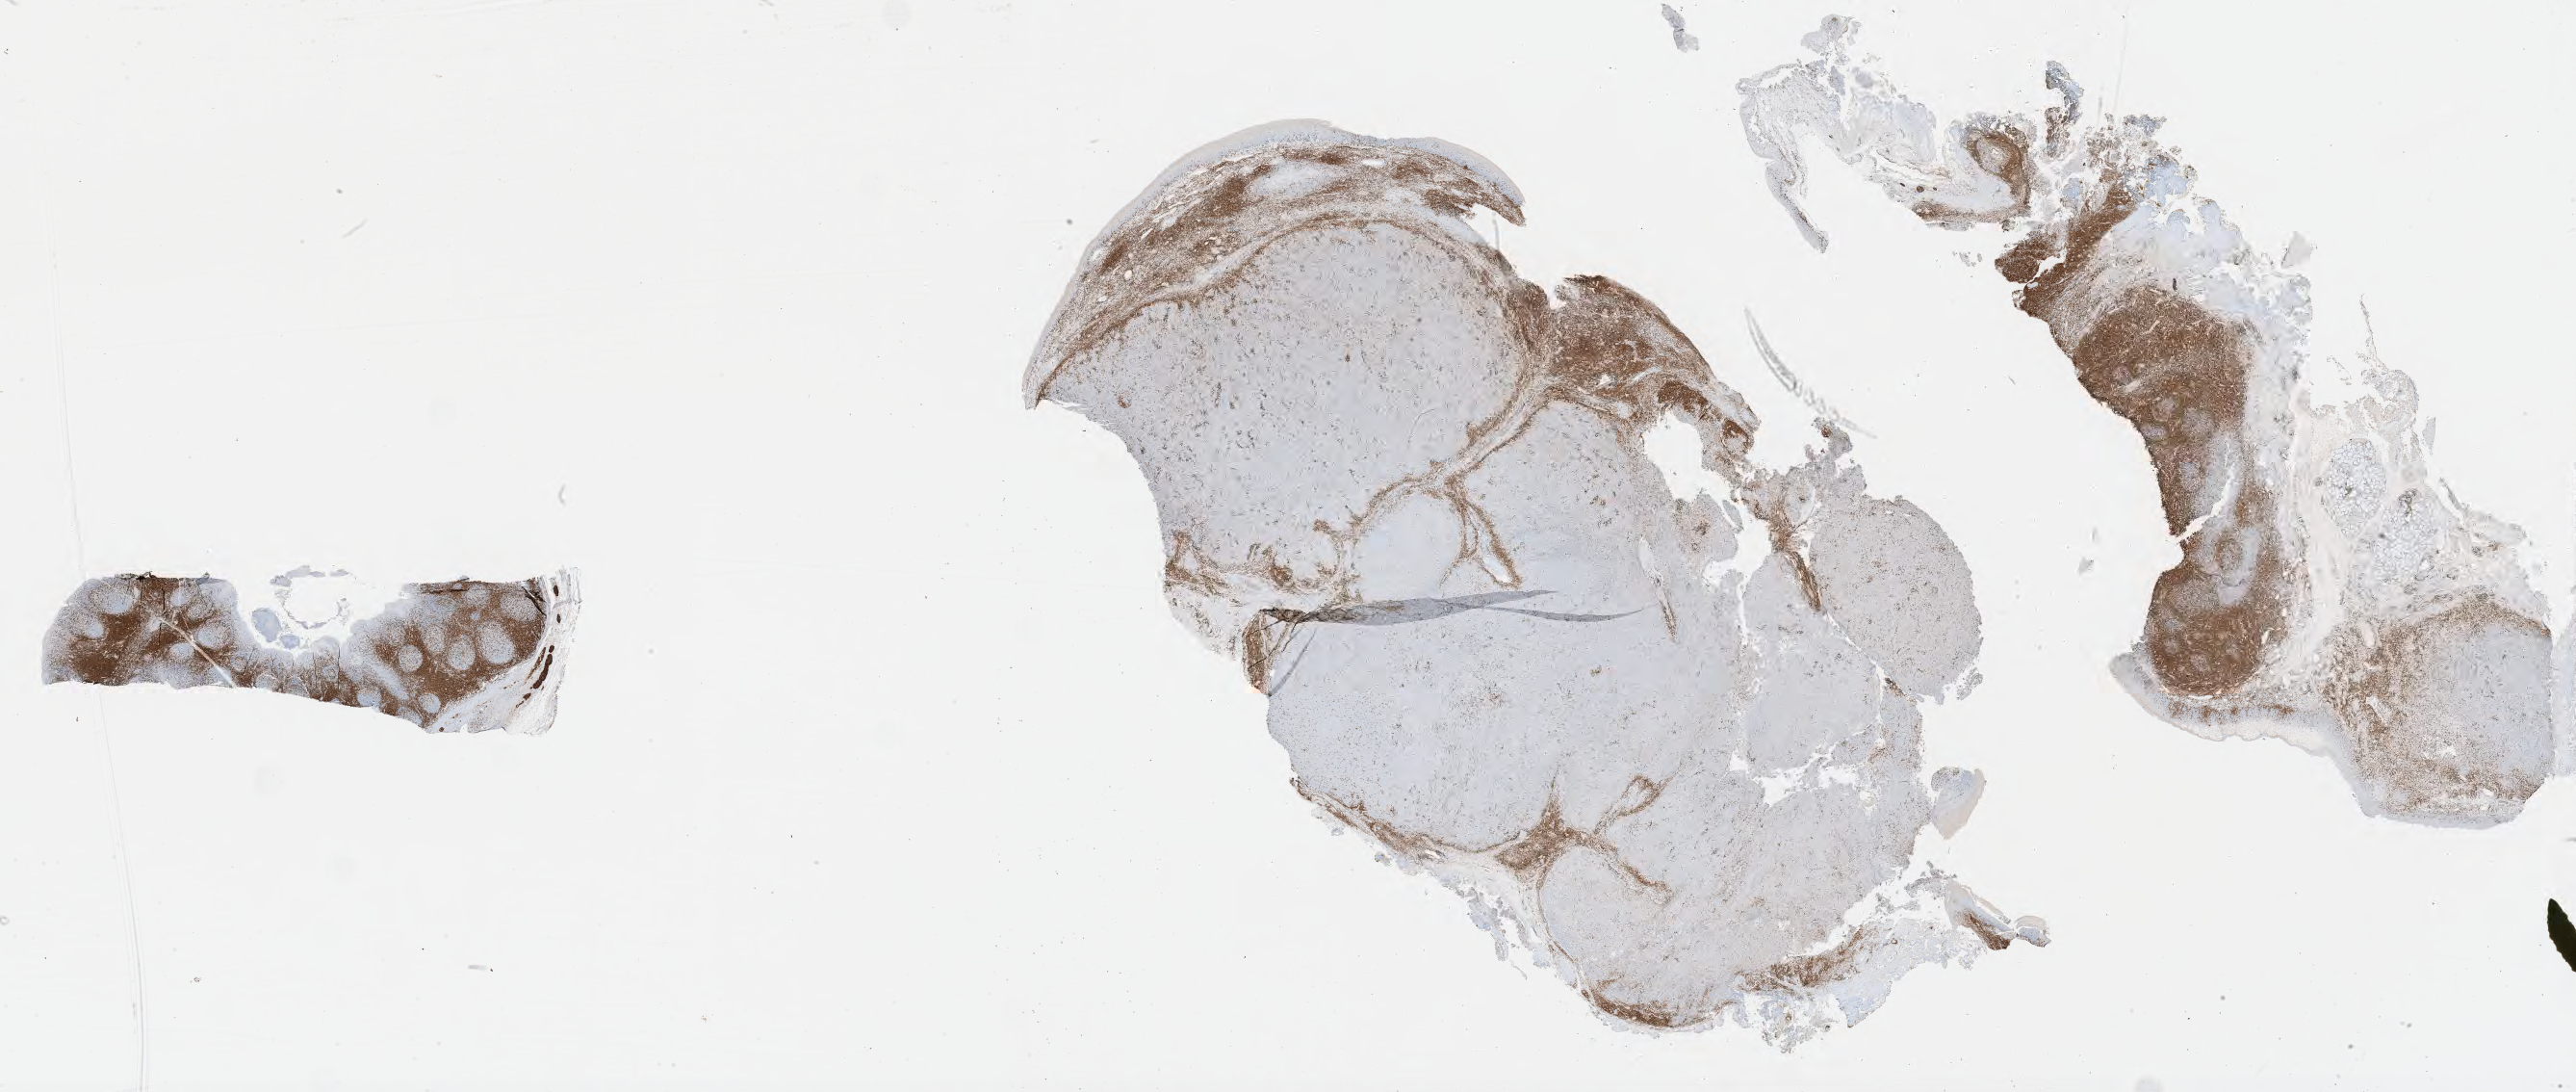
Immunohistochemistry (IHC) whole-slide image stained for CD3 — low-resolution overview of the scanned area, about 43.3 x 18.3 mm, specimen: tumor tissue, site: lymph node. Patient: male, 56 years old.
Histologic diagnosis: Diffuse large B-cell lymphoma, NOS.